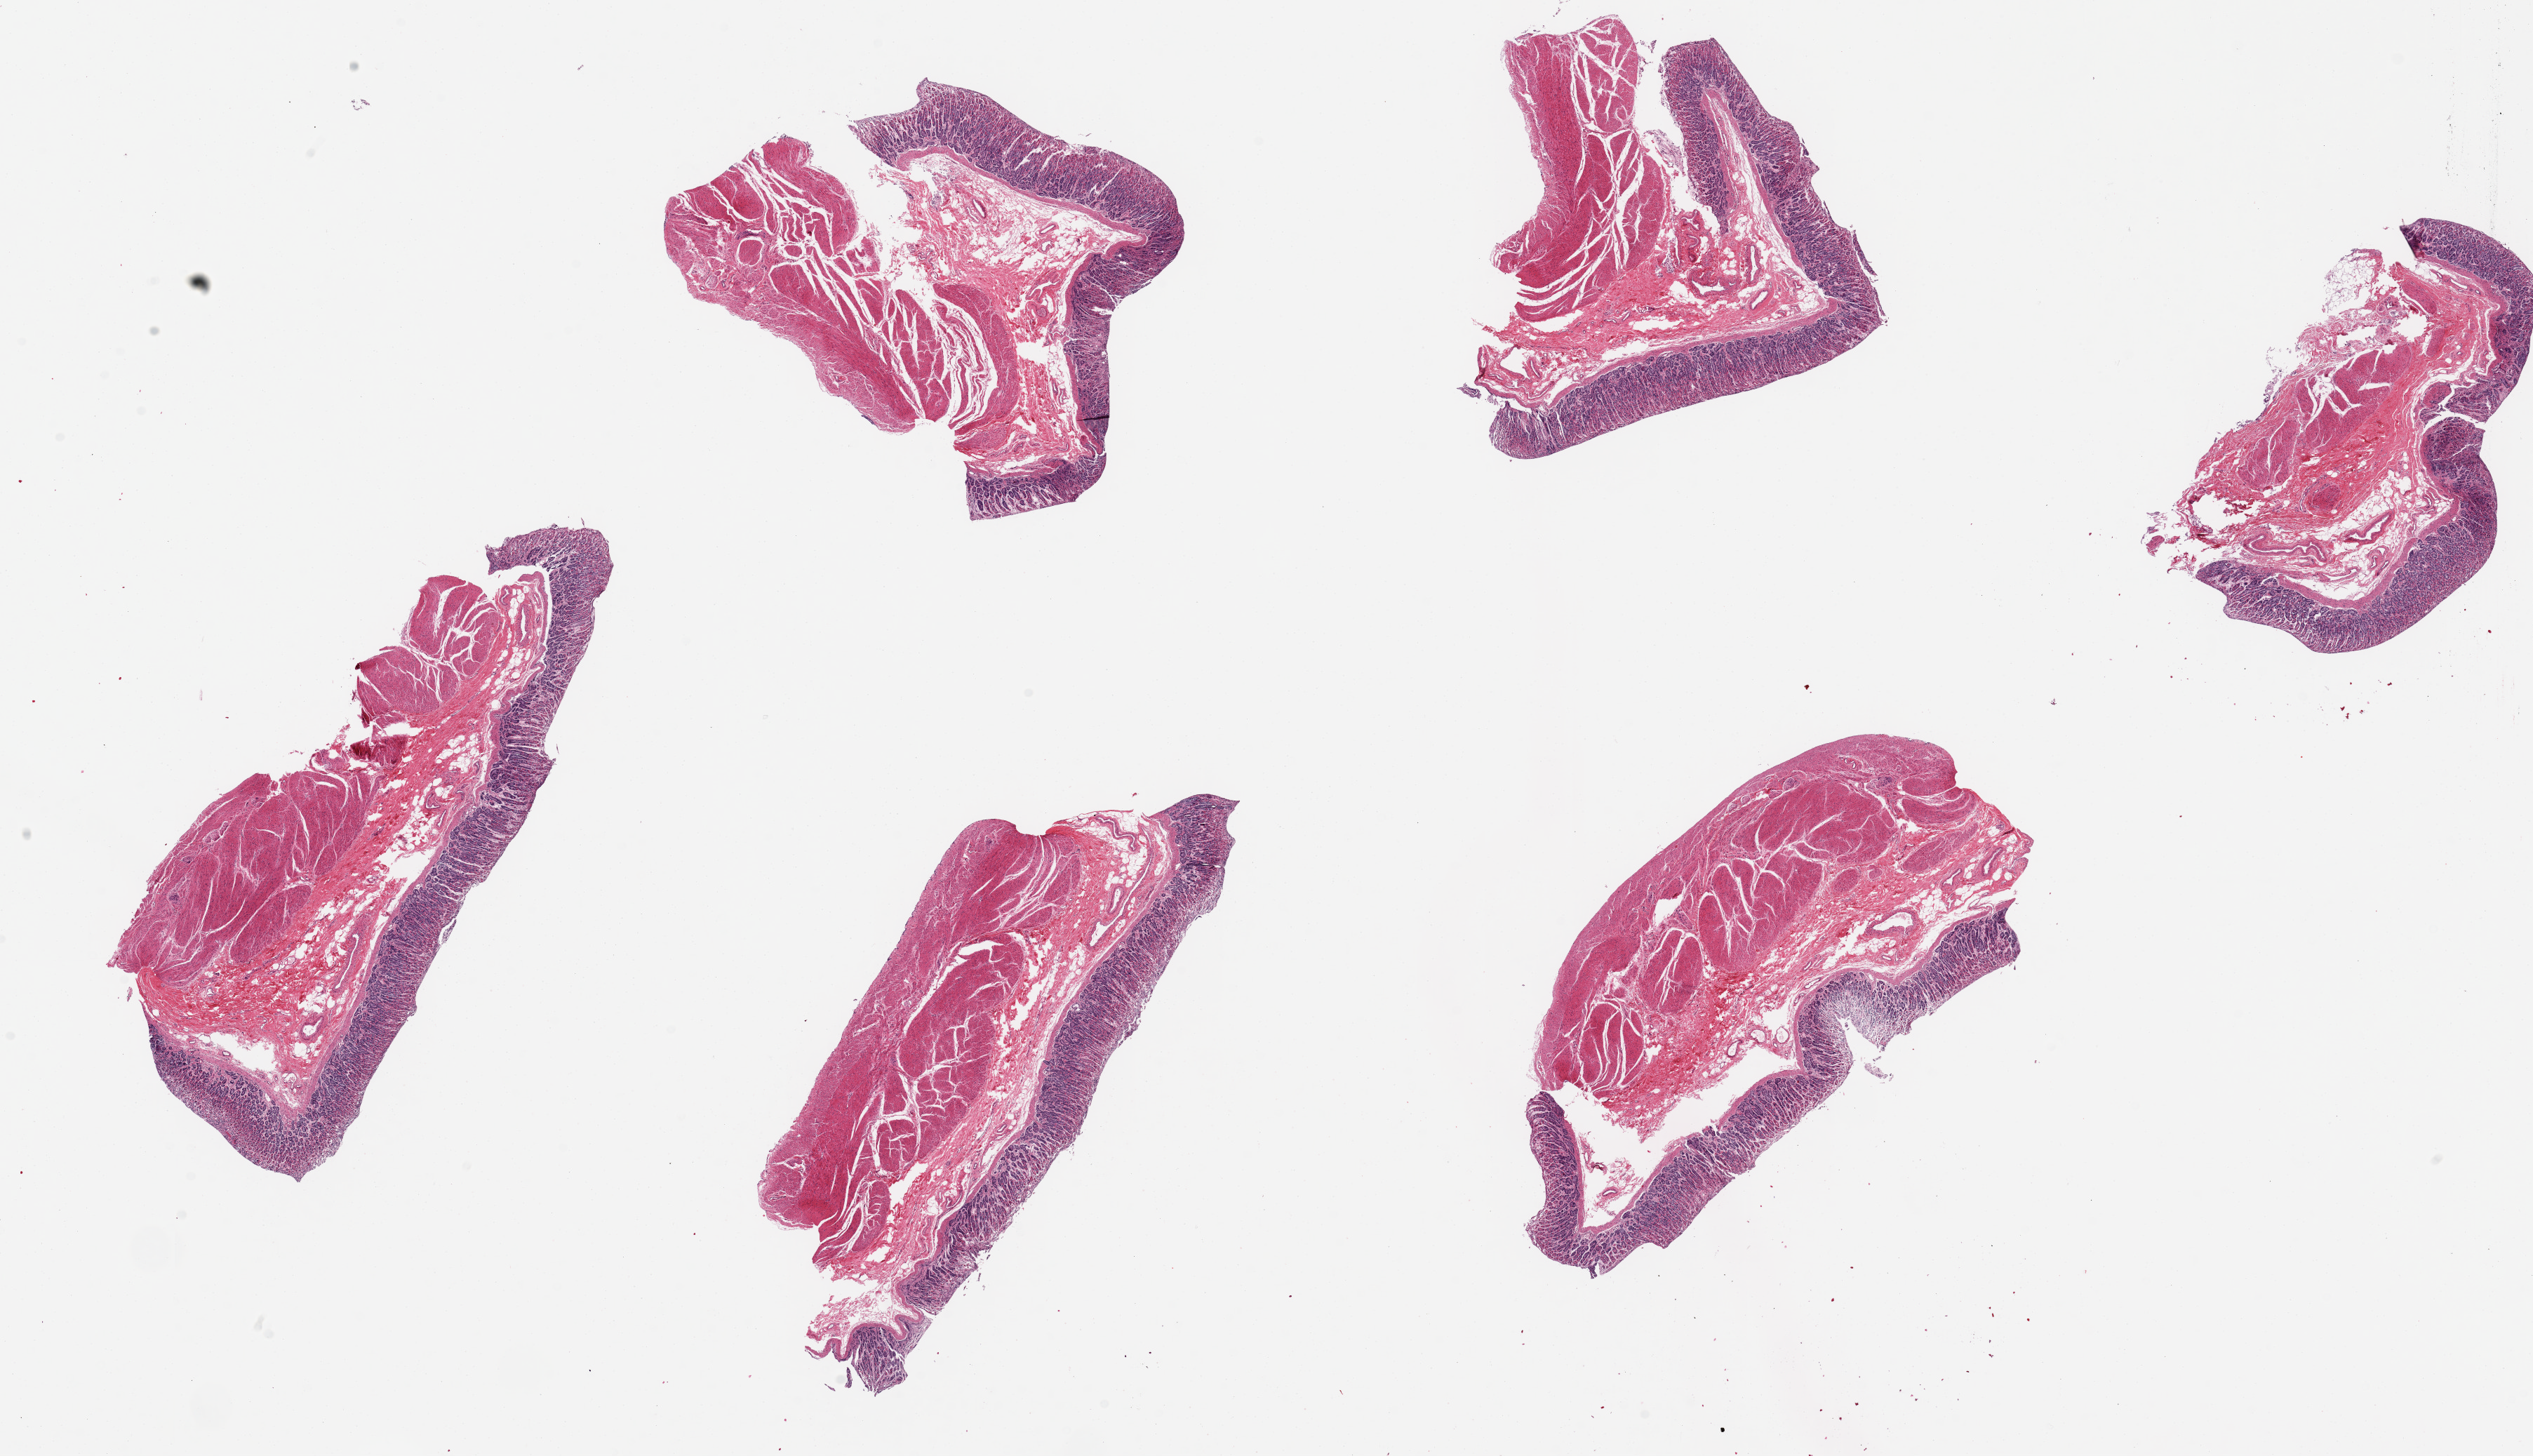
Digitized H&E-stained section — whole scanned area (about 28.5 x 16.4 mm, from a 20x scan) shown as a low-resolution overview. PAXgene-fixed, paraffin-embedded tissue. Sampled site (target tissue): stomach. Tissue donor sample. Donor: female.
* review note (as recorded): 6 pieces, up to 8x3mm; ~well preserved mucosa, ~25% thickness